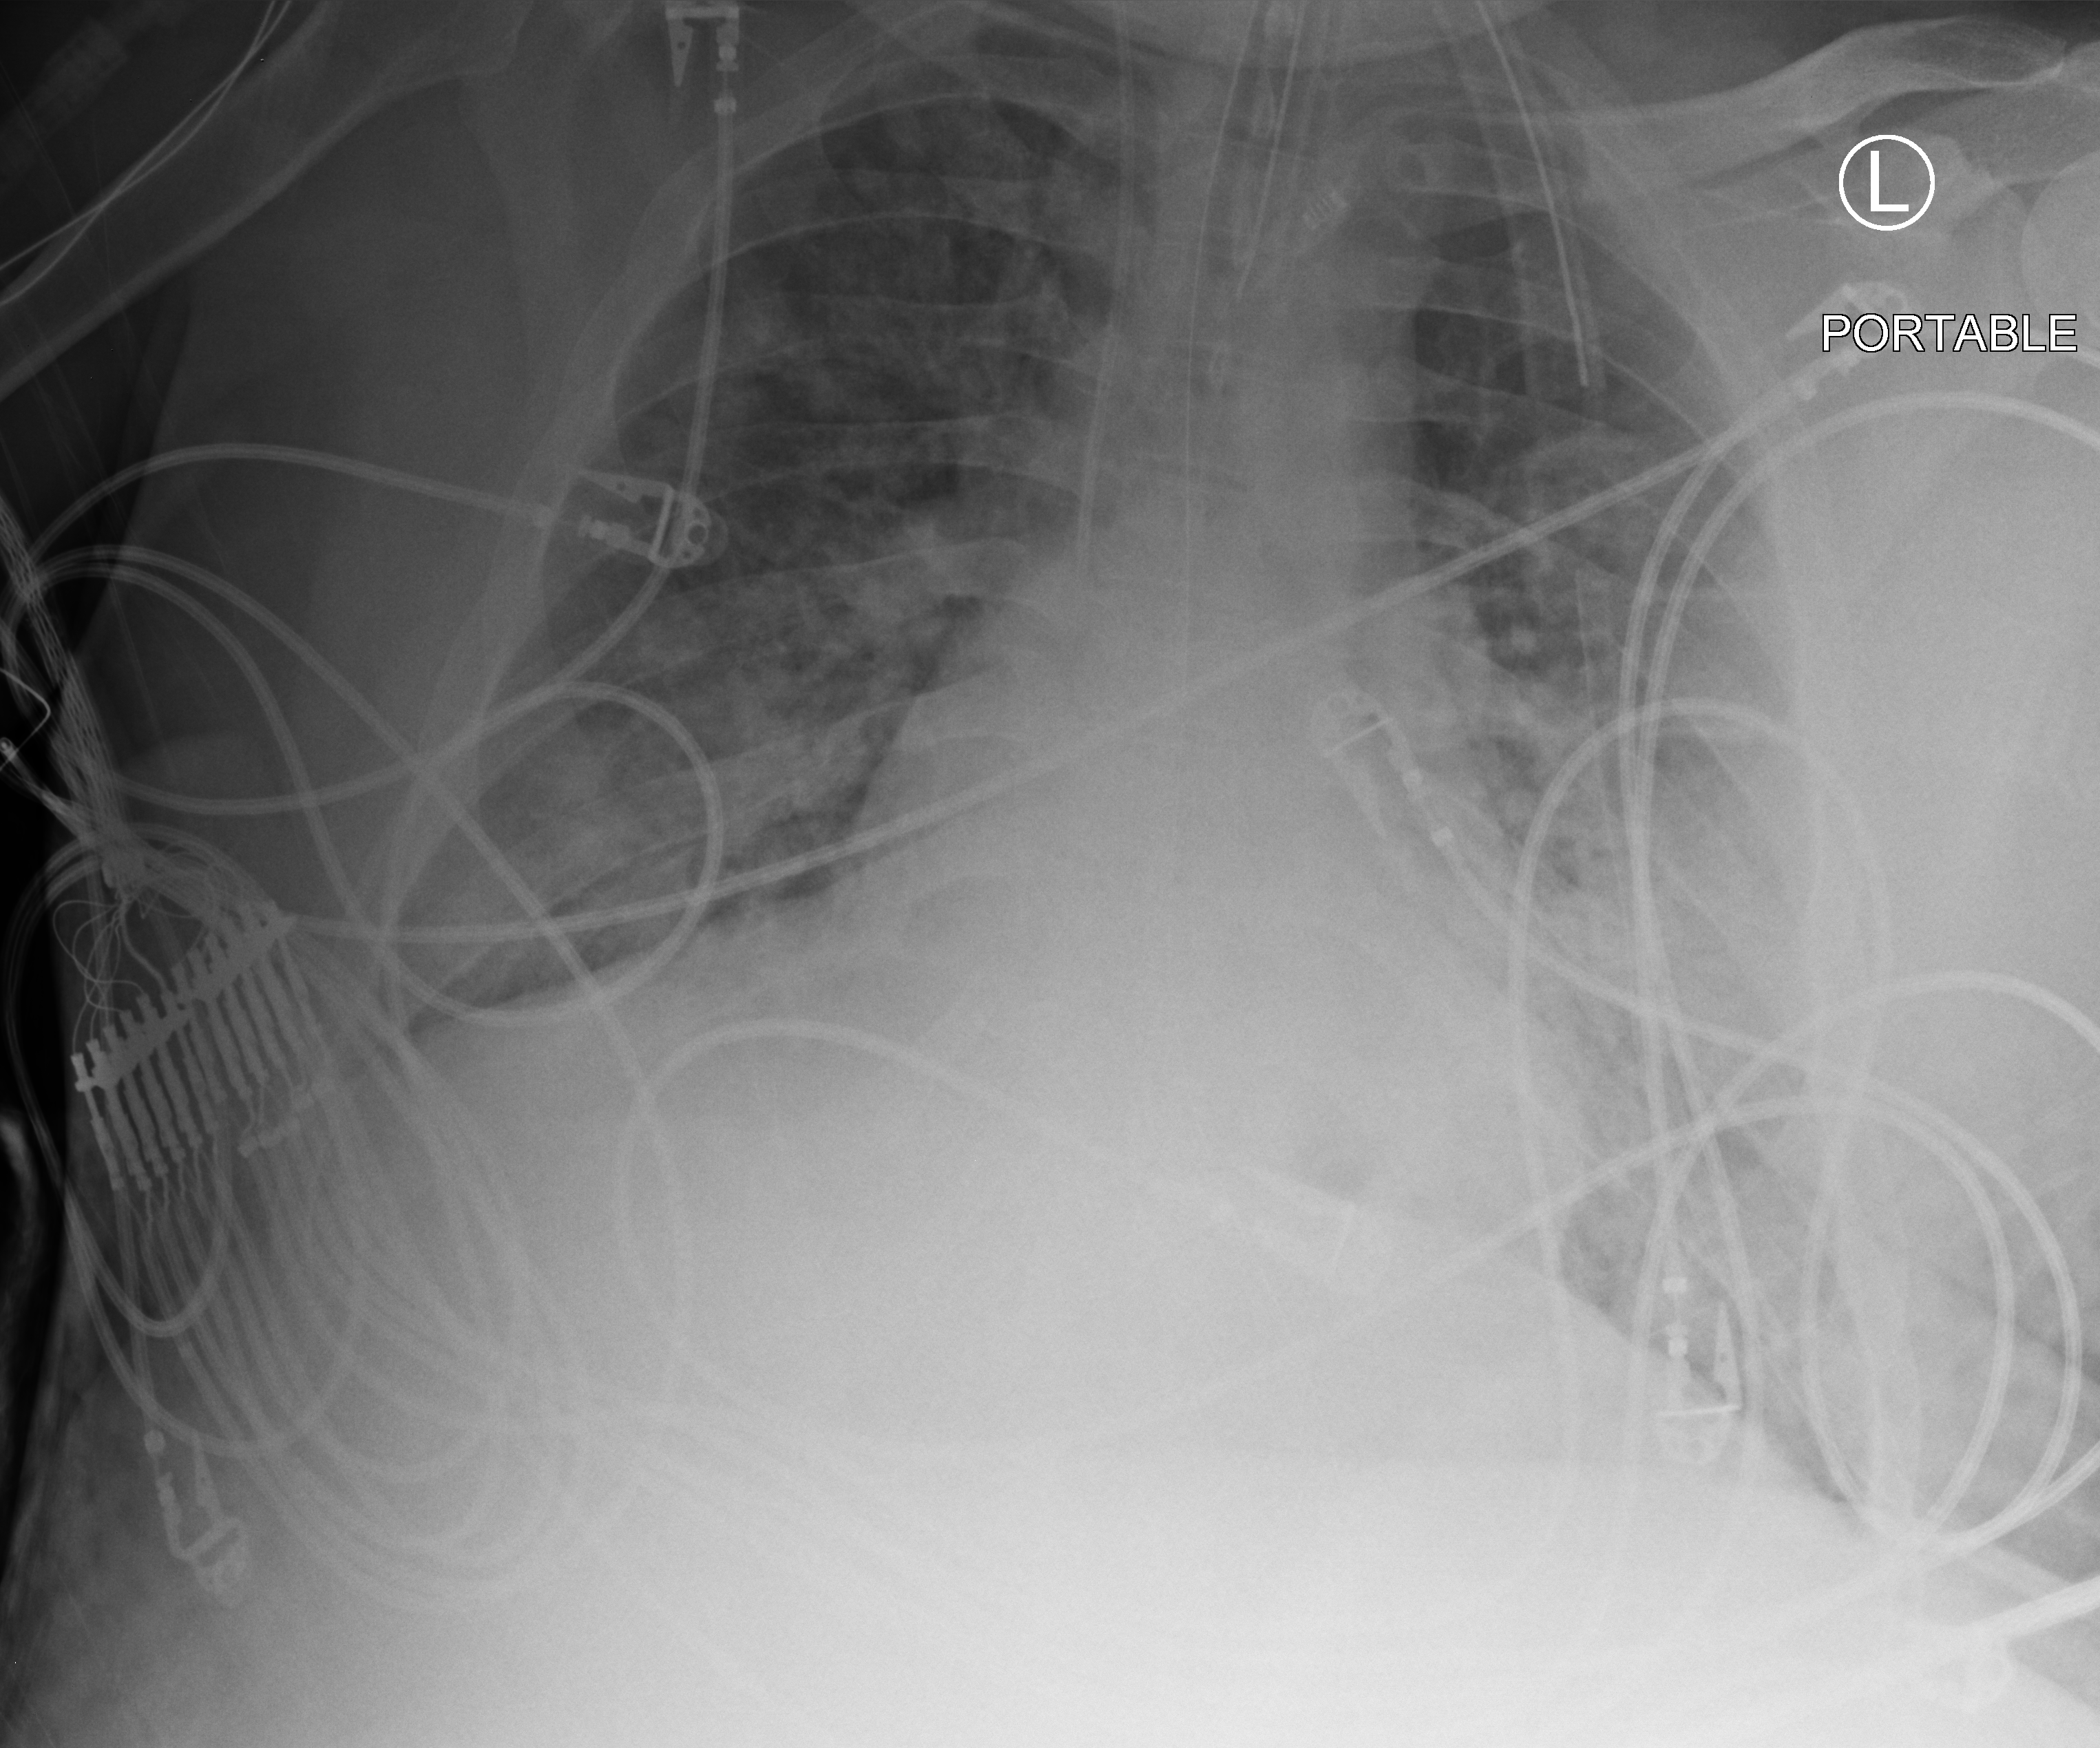
Bedside chest radiograph (computed radiography), anteroposterior (AP) projection. Adult patient hospitalised with COVID-19, age 18–59 years.
From the hospital-stay record, not from the radiograph (when in the stay this image was taken is not recorded):
- admitted to intensive care during this hospital stay: yes
- mechanically ventilated during this hospital stay: yes
- hypertension (admission record): no